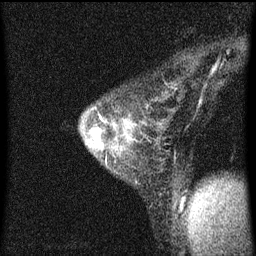
Breast MRI (dynamic contrast-enhanced), one sagittal slice. Position 43 of 60 along the scan axis. Dynamic contrast-enhanced series, image 2 of 4 at this slice position (ordered by acquisition). 1.5 T. TE 4.2 ms, TR 8 ms. 256 × 256 image matrix, field of view 180 × 180 mm. Patient: female, 33 years.
Outlined on this slice (semi-automatically segmented with operator editing):
- analysis volume of interest (the breast-tissue region the enhancement analysis was run in; not a lesion): box from (x=80, y=86) to (x=177, y=211) px
- tumour enhancement mask (voxels above the 70 % enhancement threshold inside the analysis volume of interest): (x=100, y=116)–(x=105, y=123)